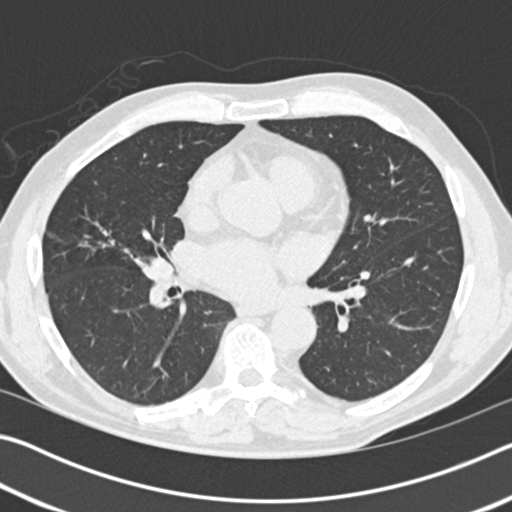
Chest CT (low-dose screening protocol), one axial image; baseline annual screen; lung window (W 1500 / L -600 HU); 2 mm slice thickness; standard (soft-tissue) reconstruction kernel (B30f); slice 88 of 193 in the series; 512 × 512 image matrix. Male participant, aged 57 years at enrolment. Former smoker at enrolment.
Lesion marked by an expert reader, bounding box (x1, y1, x2, y2) in pixels: (144, 249, 181, 284). The screening reader recorded 2 non-calcified nodules or masses ≥4 mm on this exam (right middle lobe, right middle lobe); which of them this box marks is not recorded. Official screen result: positive, change unspecified: nodule(s) >= 4 mm or enlarging nodule(s), mass(es), or other non-specific abnormalities suspicious for lung cancer. Participant outcome: lung cancer diagnosed 784 days after this screen (after the third annual screen) — carcinoid tumor, NOS, right middle lobe, carcinoid, stage not assessed, 15 mm at pathology.